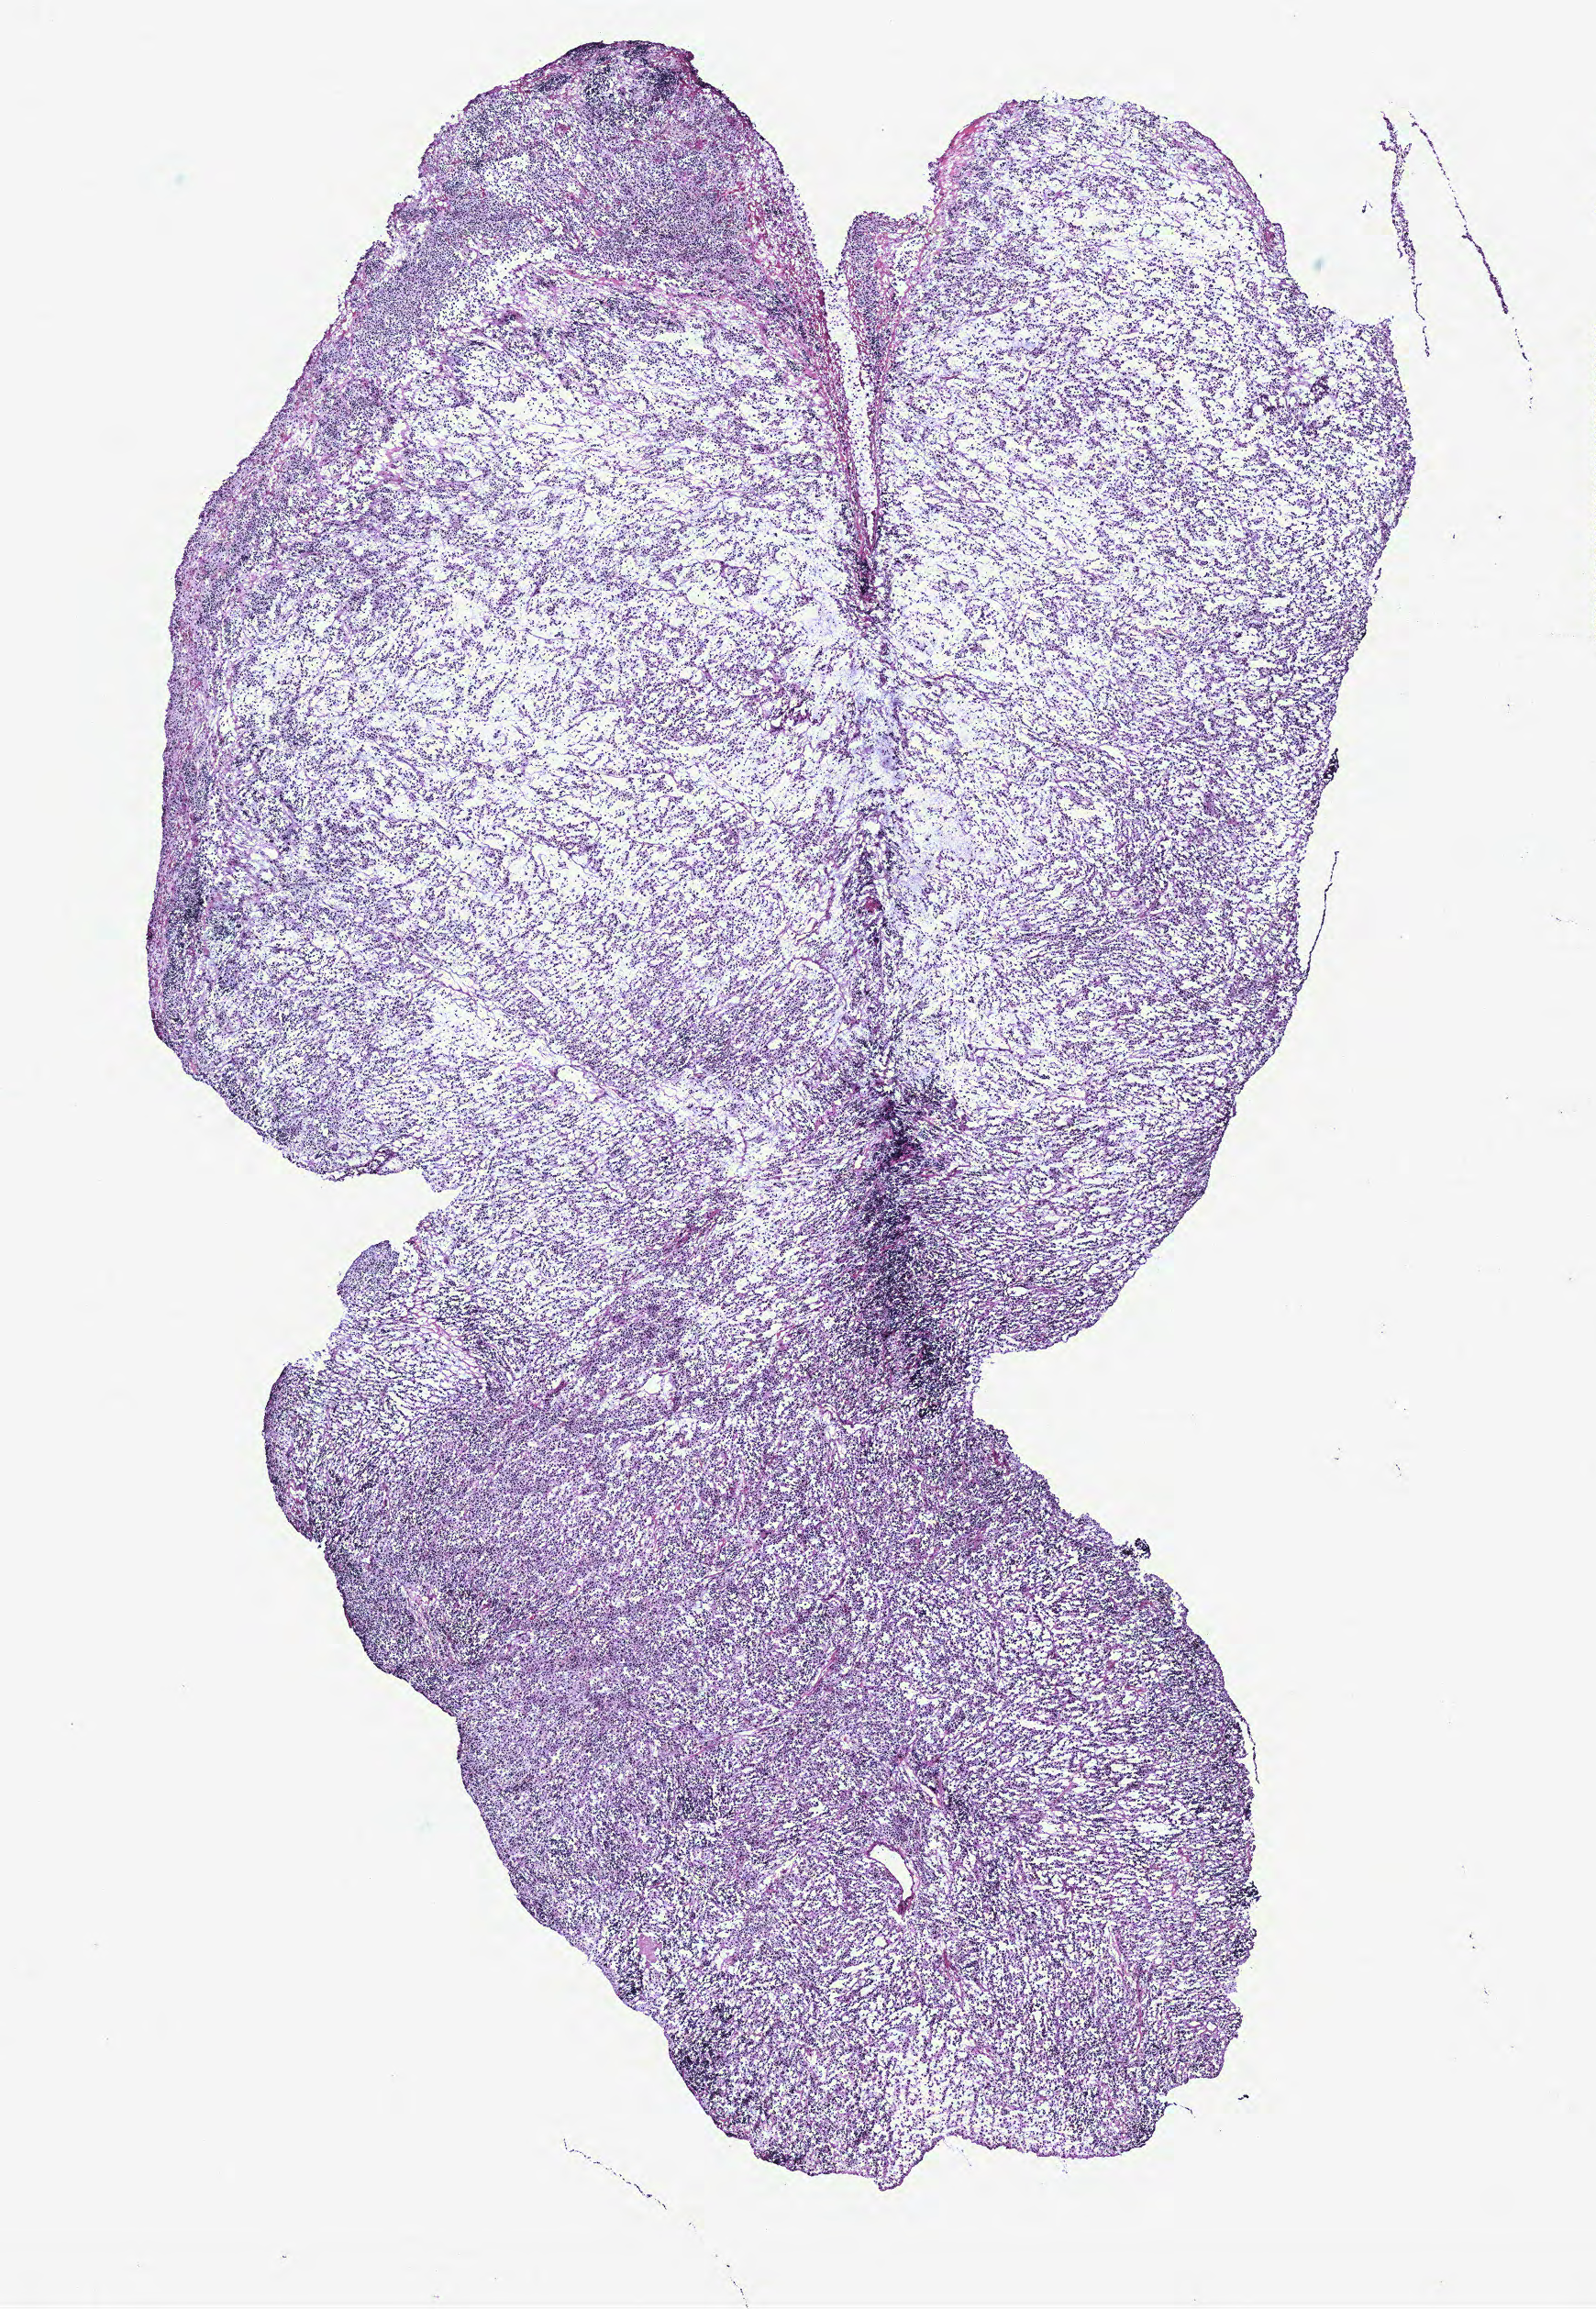
H&E-stained whole-slide image, a low-resolution overview of the entire scanned area, about 7.0 x 10.1 mm. Ovary, tumour tissue. Patient: female, age 65 years.
Histologic diagnosis: Serous adenocarcinoma, NOS. Primary tumour site (as recorded): ovary.